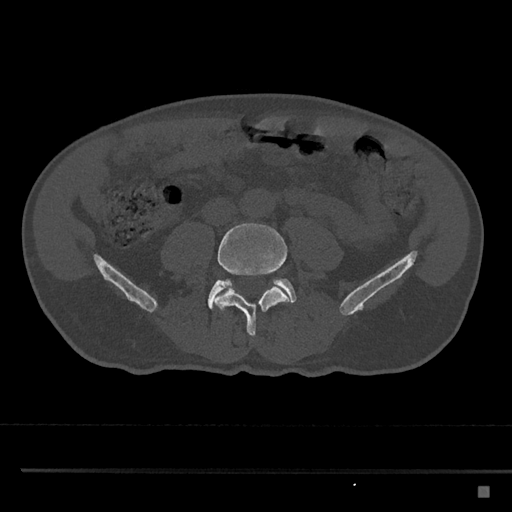
CT including the spine, one axial slice. Position 619 of 797 along the scan axis. Reconstruction kernel Br40s/3. 120 kVp. Bone window (W 1800 / L 400 HU). 0.5 mm slice thickness. 512 × 512 image matrix, field of view 391 × 391 mm. Male patient, age 59 years. From the clinical record (not read from this slice): primary cancer: prostate.
Structures marked on this image (semi-automatic segmentation, software-assisted and operator-edited):
- L4 vertebra: bounding box (x1, y1, x2, y2) in pixels: (215, 223, 290, 336)
- L5 vertebra: (208, 278, 297, 310)